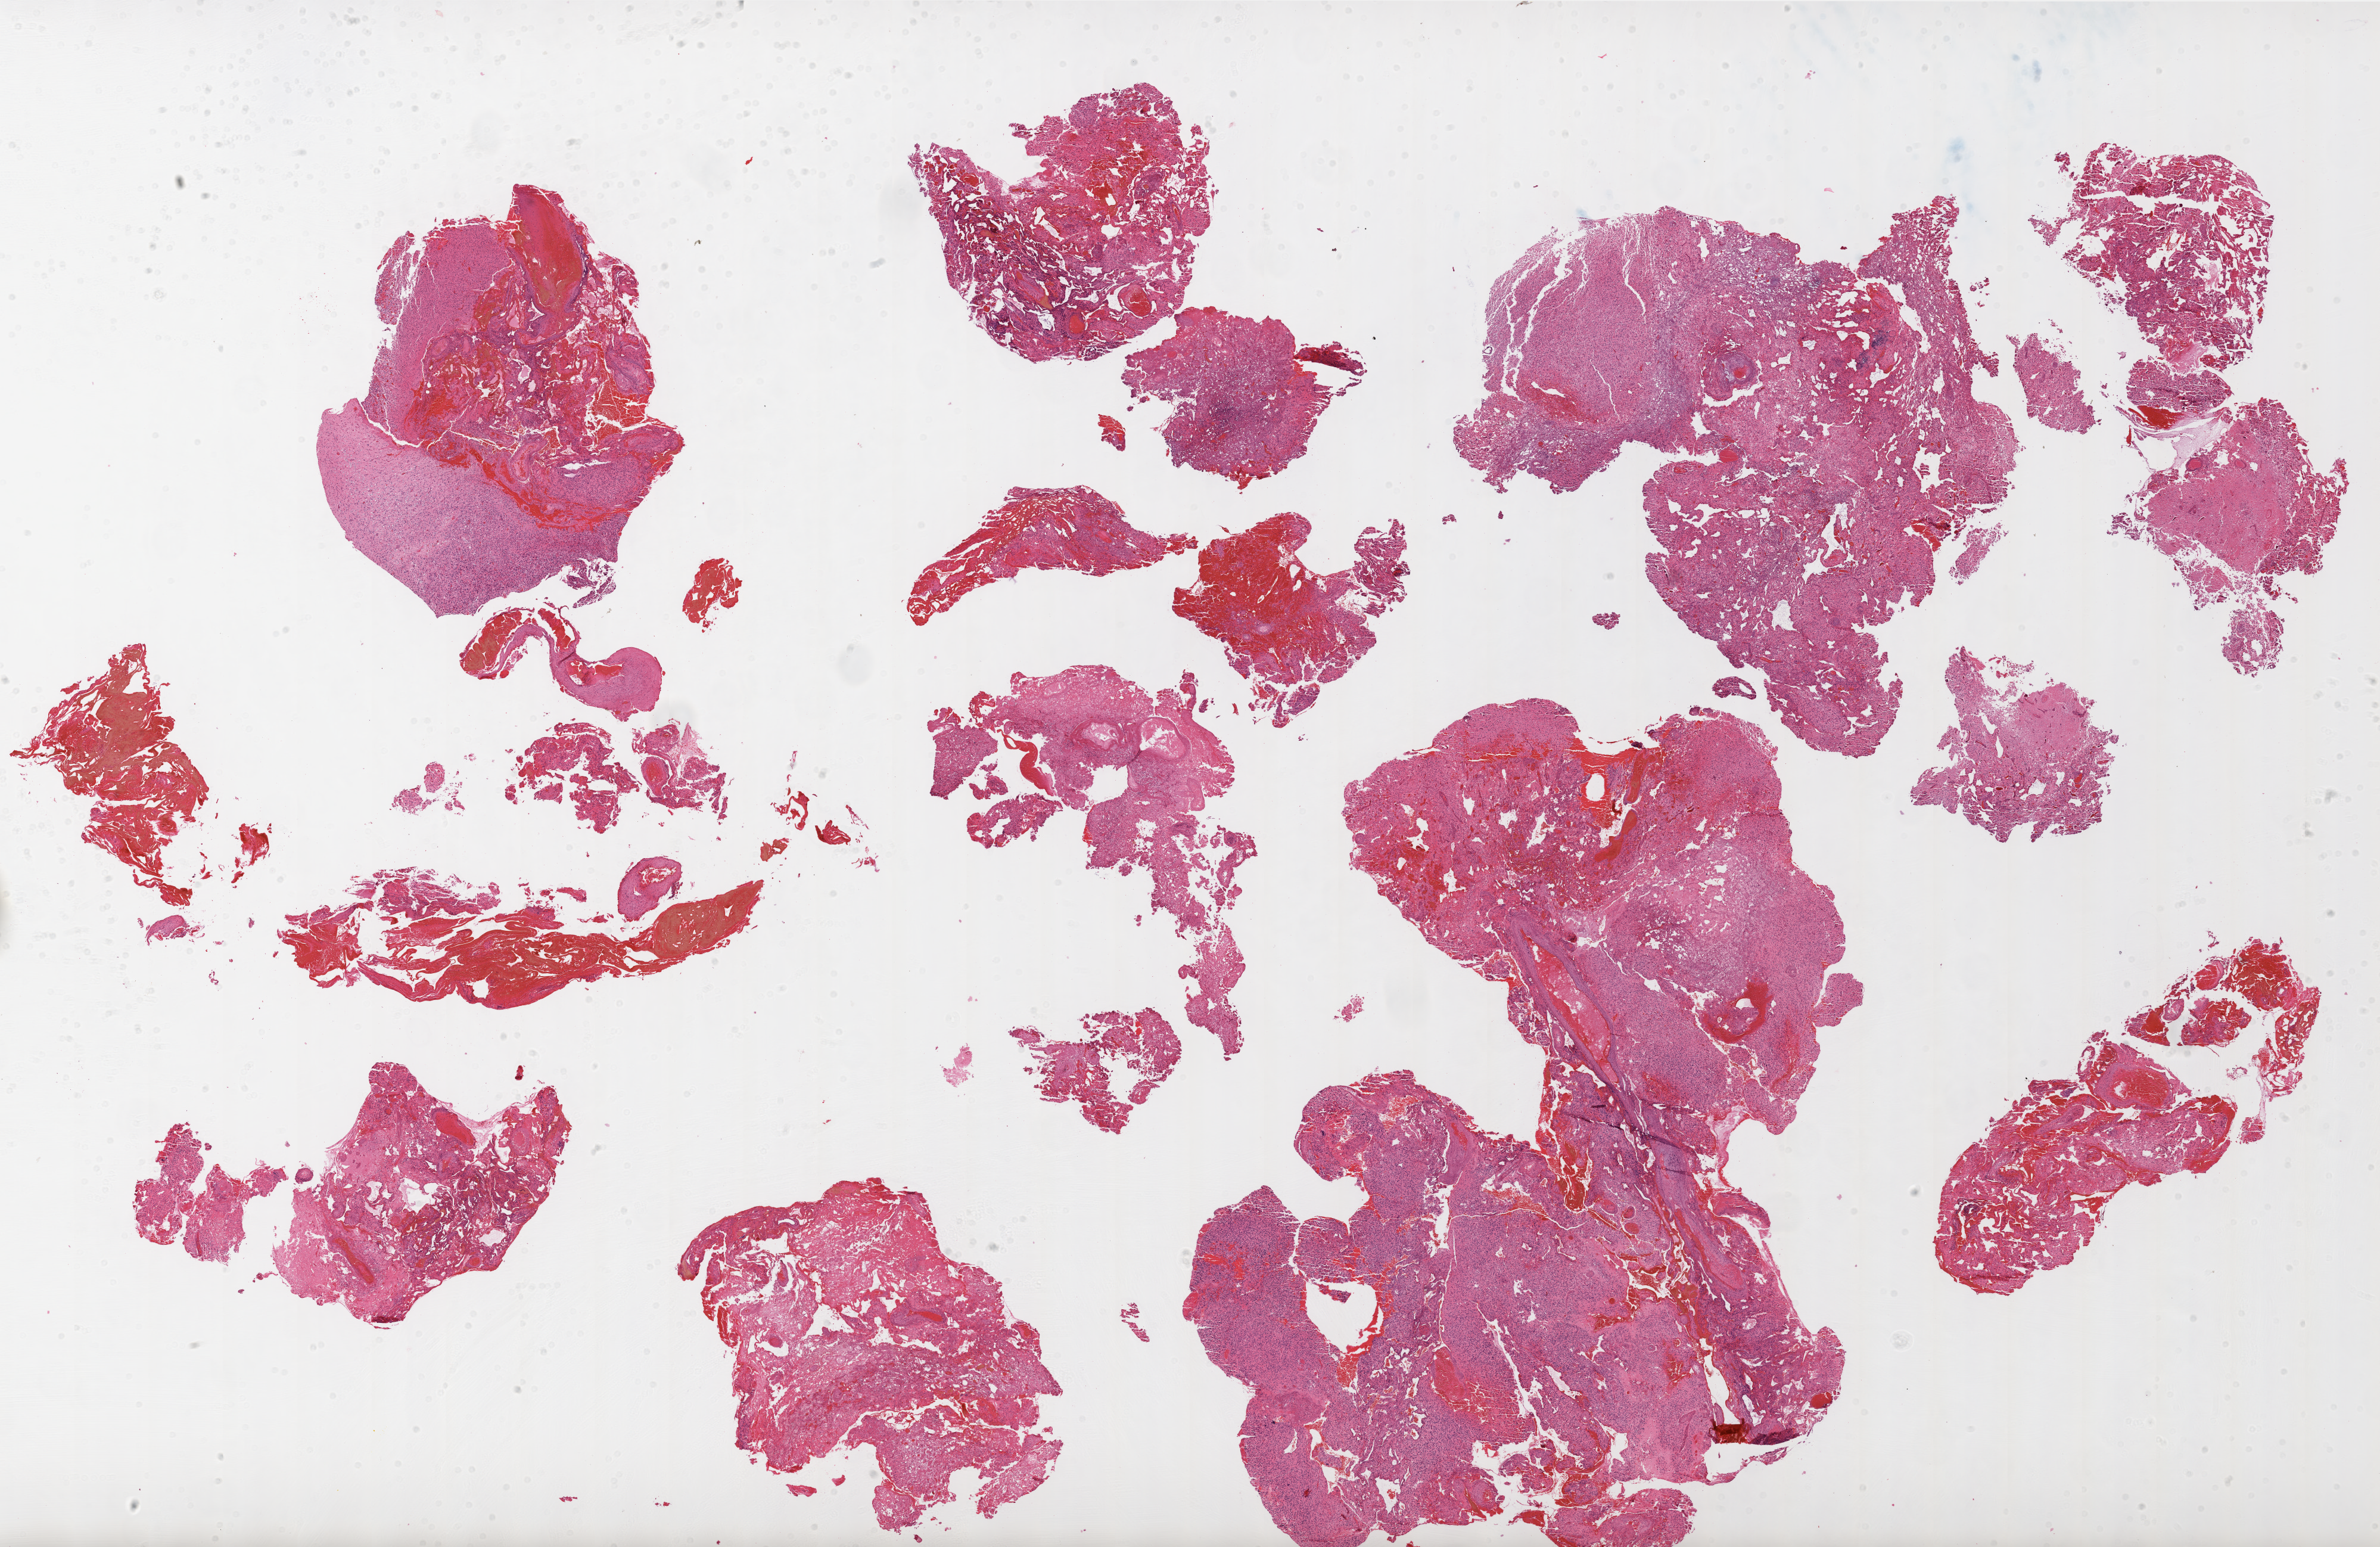
Whole-slide histology image, Hematoxylin and eosin (H&E) stained, shown as a low-resolution overview of the whole scanned area (about 32.0 x 20.8 mm), formalin-fixed paraffin-embedded (FFPE) diagnostic section, brain, primary tumour sample. Male patient; age at initial diagnosis 76 years.
Diagnosis: Glioblastoma.